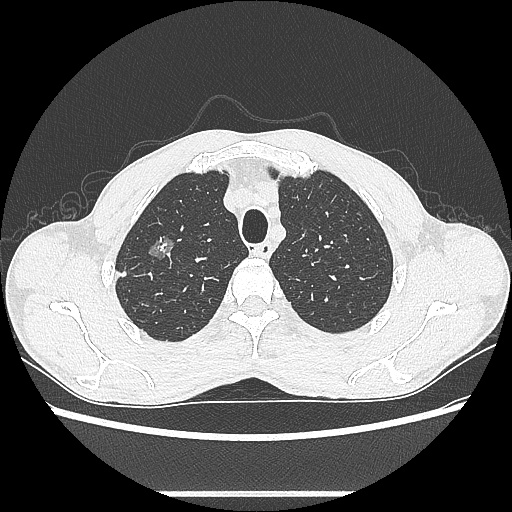
Chest CT, one axial slice; slice 490 of 601 in the series (ordered by position); reconstruction kernel LUNG; lung window (W 1500 / L -600 HU); 0.62 mm slice thickness; 512 × 512 image matrix, field of view 357 × 357 mm. Patient: male, 54 years. Case-level facts recorded for this patient, not image findings: clinical TNM (as recorded): T1a N0 M0.
Structures marked on this image (rectangle marked by the reading radiologist):
- lung tumour (recorded histology: adenocarcinoma): bounding box [x1, y1, x2, y2] px = [143, 229, 179, 262]